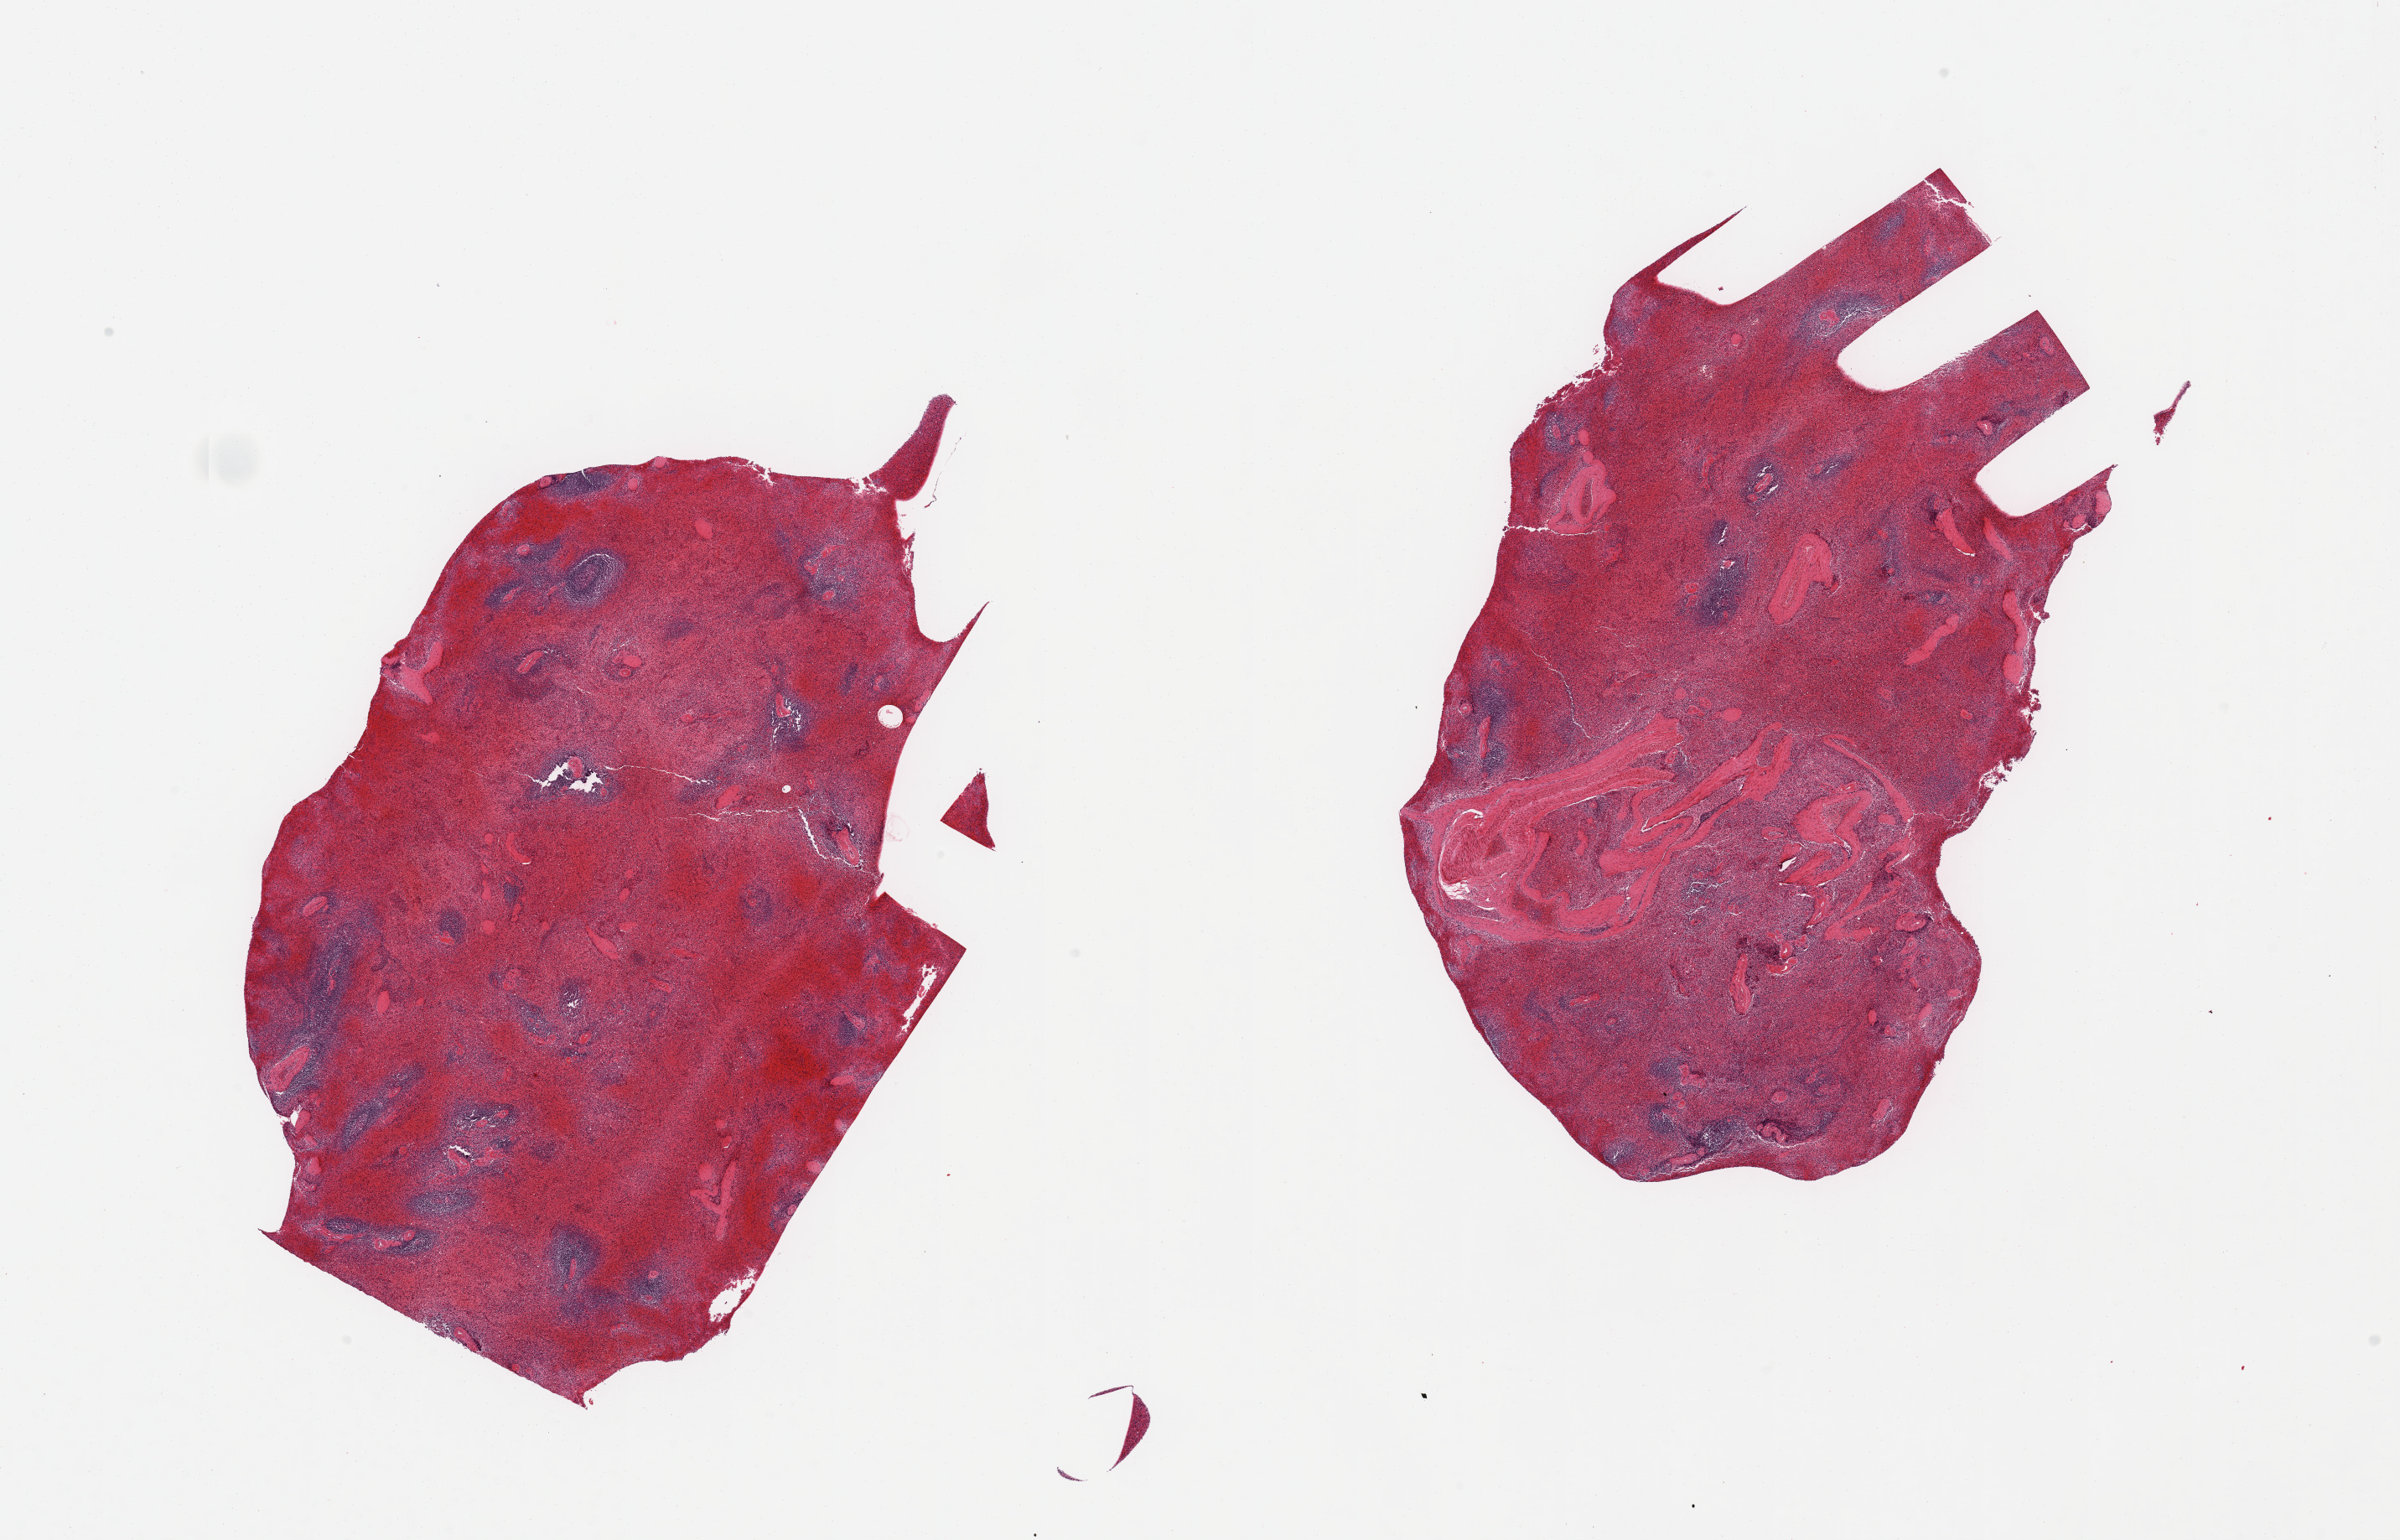
Whole-slide image, hematoxylin and eosin (H&E) stain, brightfield, low-resolution overview of the scanned area, about 22.6 x 14.5 mm (from a 20x scan), PAXgene-fixed paraffin-embedded (PFPE) section, section of spleen (target tissue), tissue donor sample.
* pathologist's review note for this sample: 2 pieces, marked congestion